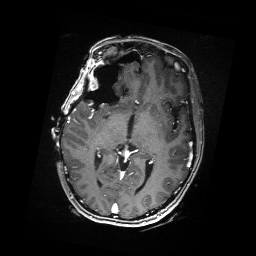
Brain MRI from a brain-tumour surgery series, one axial slice; position 96 of 176 along the scan axis; T1-weighted post-contrast; 1 mm slice thickness; 256 × 256 image matrix, field of view 256 × 256 mm. Case-level facts recorded for this patient, not image findings: histopathology: Metastatic Carcinoma from Breast primary; tumour location: Right Frontal.
Structures marked on this image (manually delineated by an expert):
- residual tumour: bounding box [x1, y1, x2, y2] px = [97, 69, 109, 88]